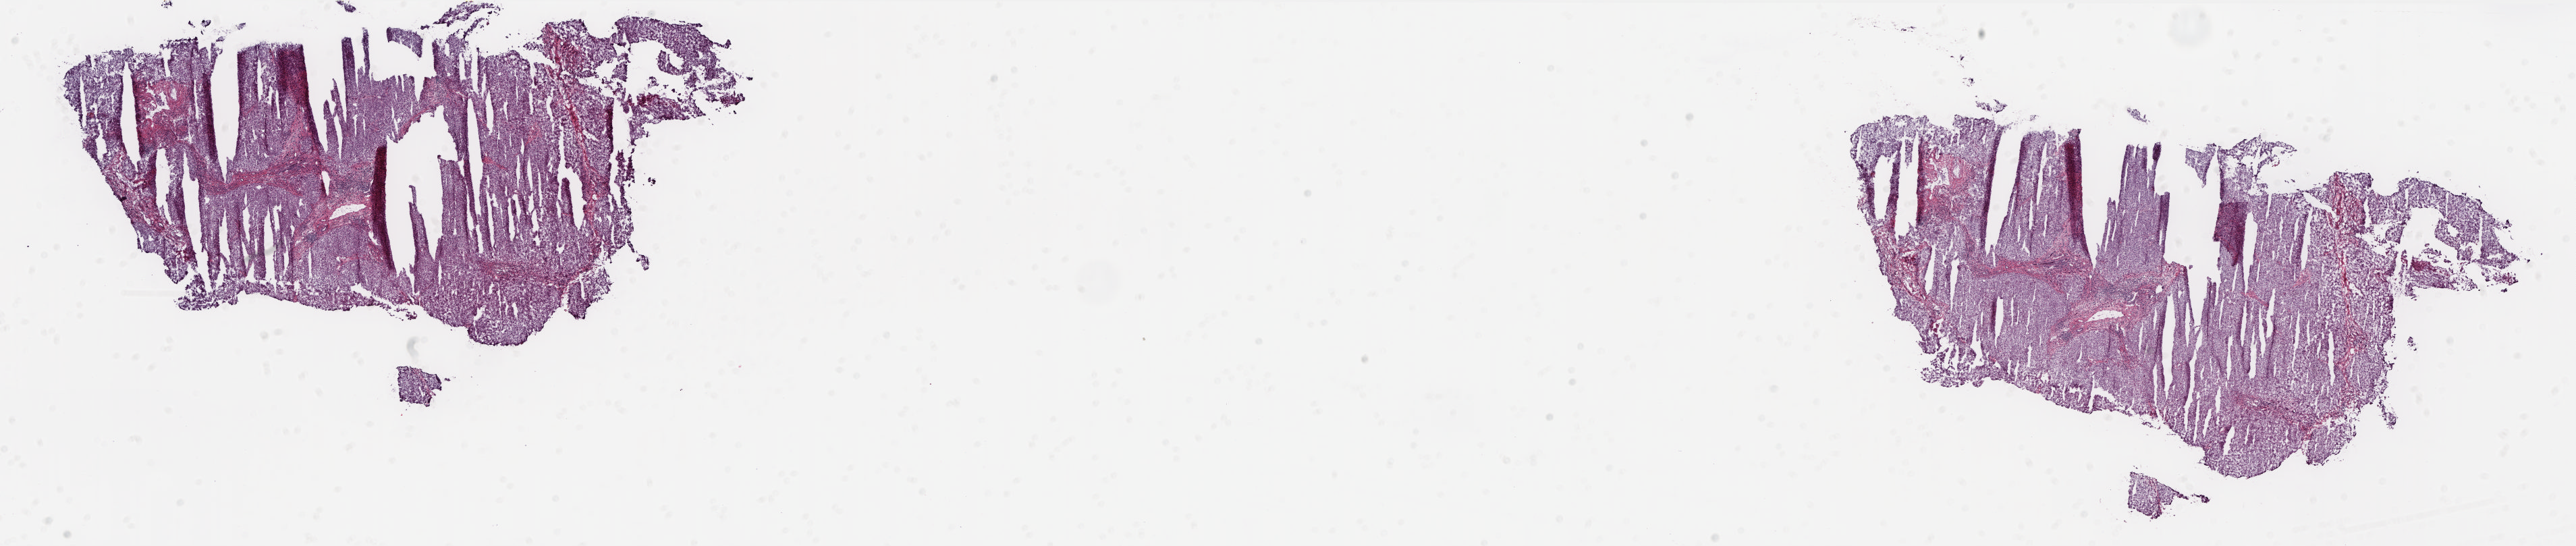
Digitized Hematoxylin and eosin (H&E) stained tissue section (whole slide) — a low-resolution overview of the entire scanned area, about 30.8 x 6.5 mm, frozen section from the top of the tissue portion, solid tissue normal (non-tumour tissue) sample from the liver. Patient: male, age at initial diagnosis 66 years. Slide review estimates, as recorded: tumour cells 0%, tumour nuclei 0%, normal cells 82%, stromal cells 18%, necrosis 0%. Inflammatory infiltration, as recorded: lymphocyte infiltration 8%, monocyte infiltration 1%, neutrophil infiltration 0%.
This section: solid tissue normal (non-tumour) sample from the same patient. Patient diagnosis: Hepatocellular carcinoma, NOS.